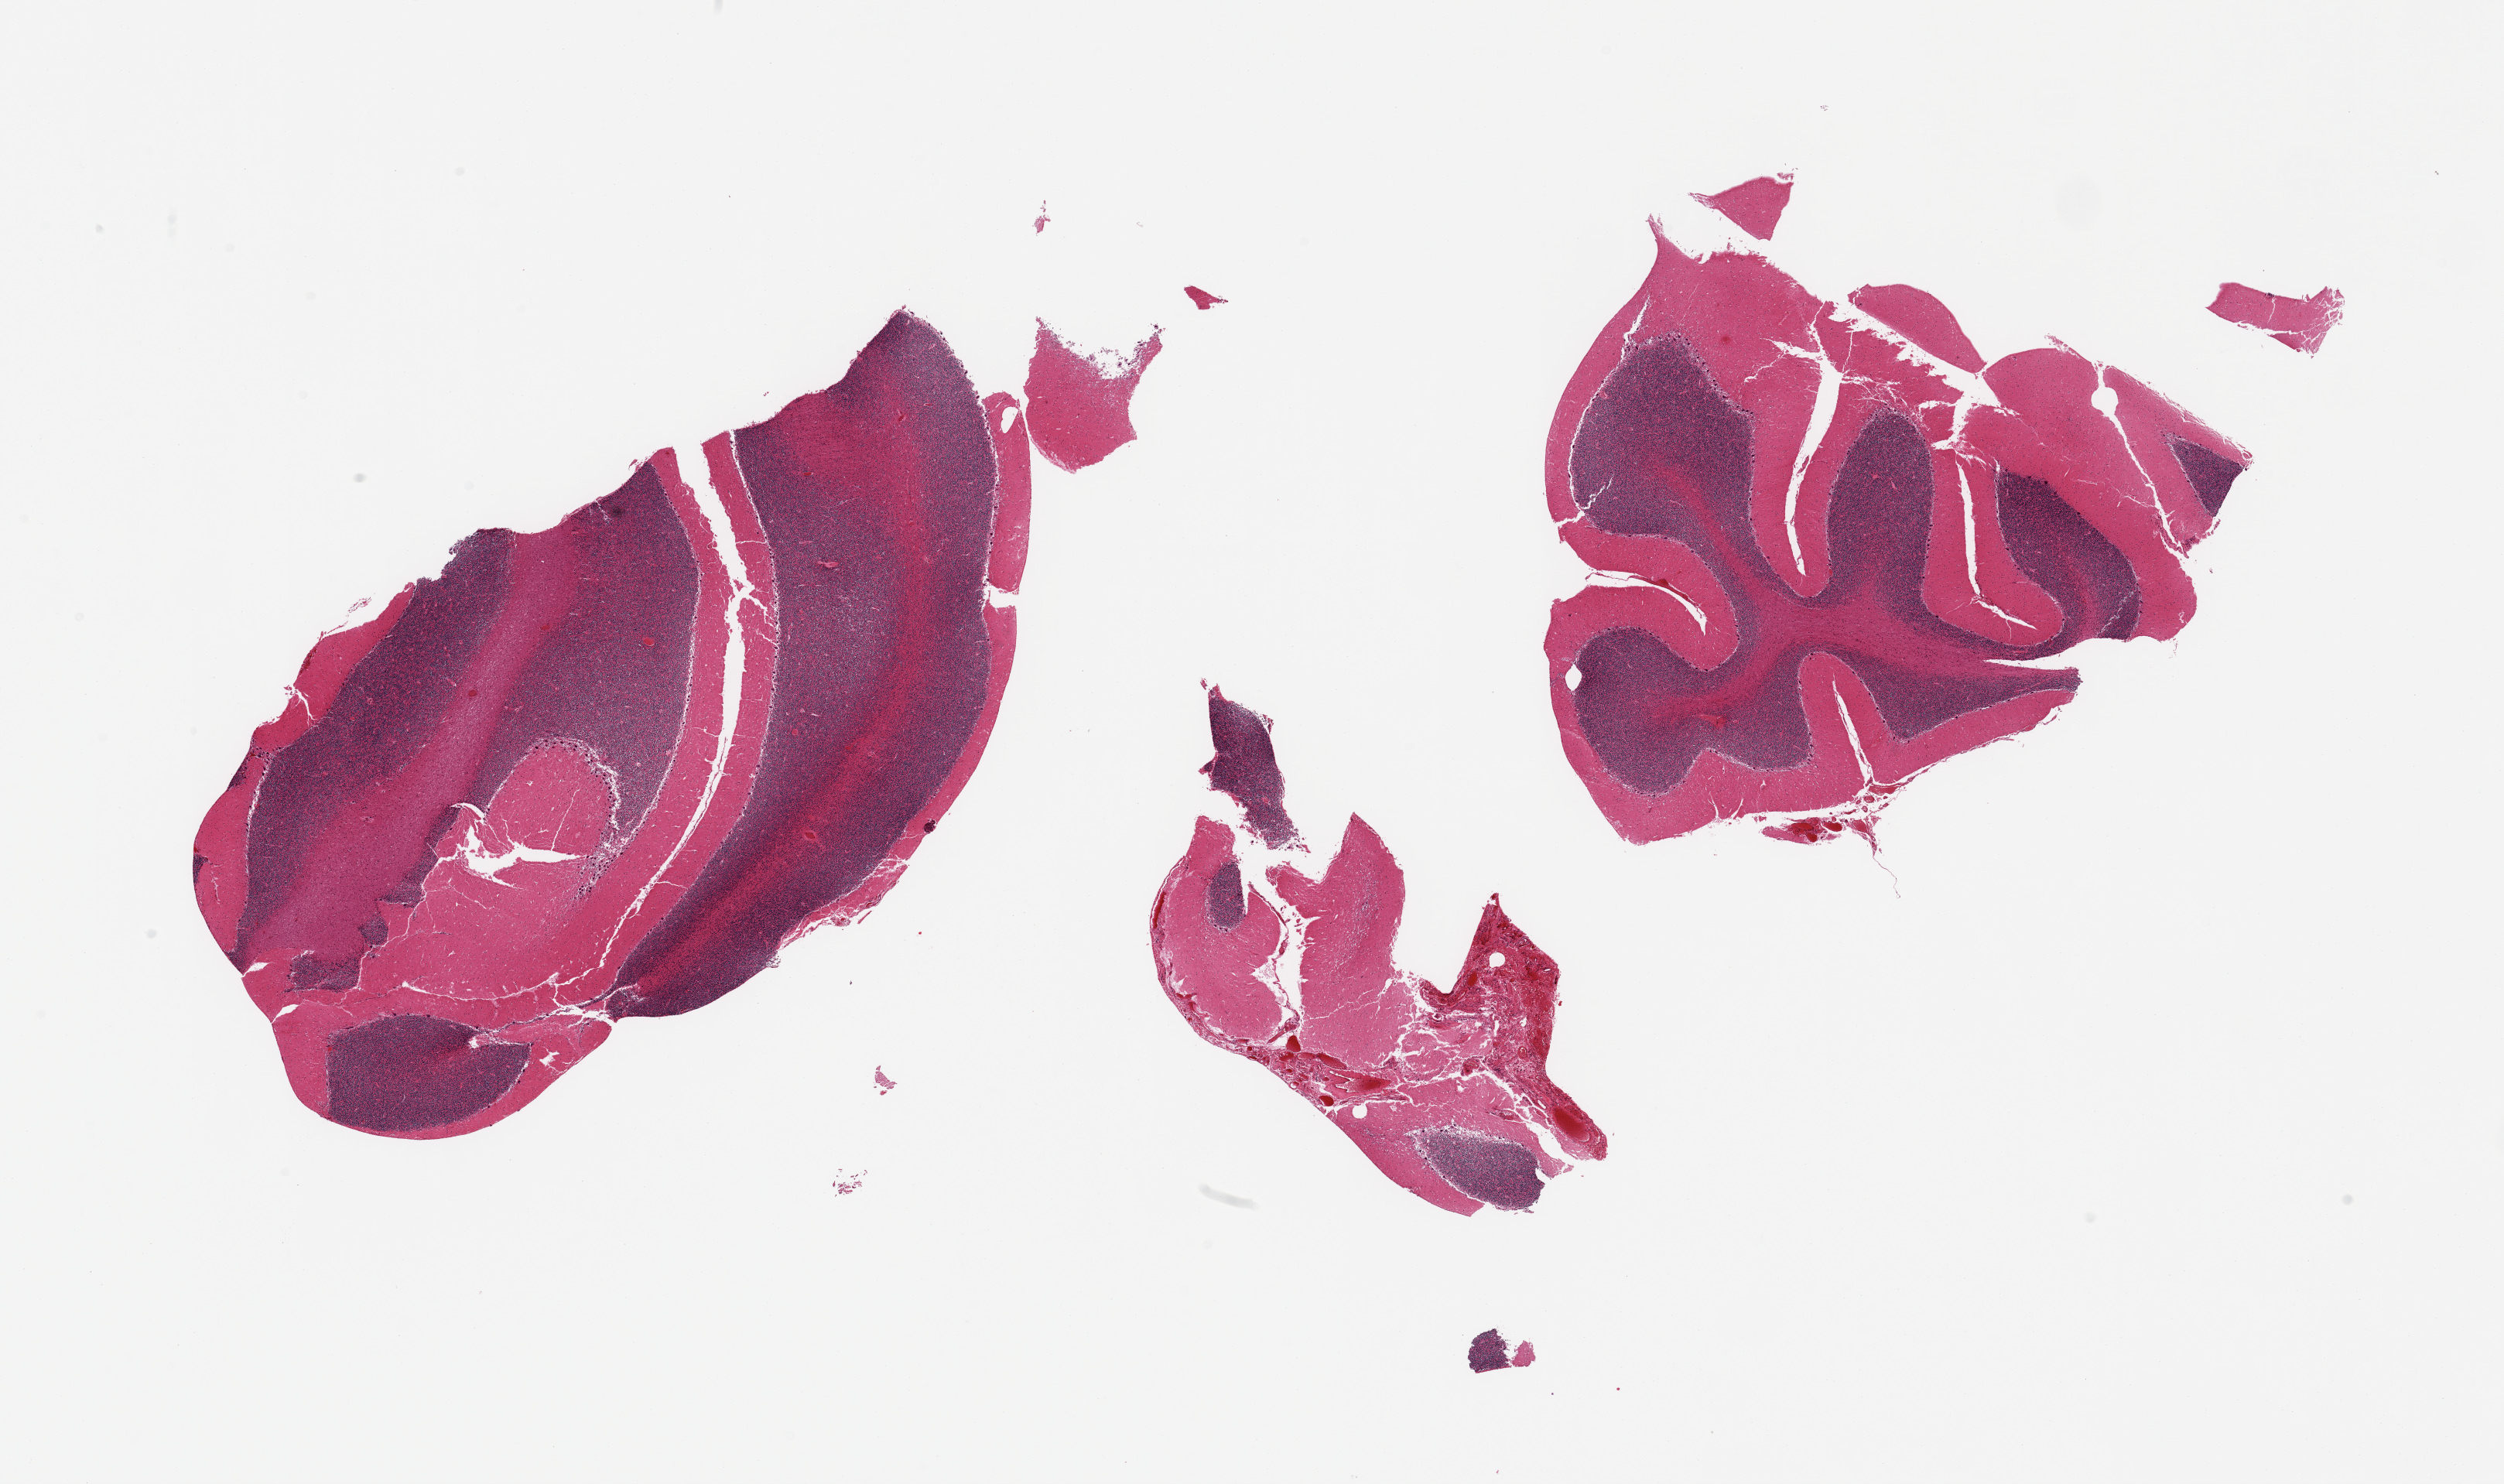
Digitized haematoxylin and eosin-stained section, brightfield, low-resolution overview of the scanned area, about 25.6 x 15.2 mm; PAXgene-fixed, paraffin-embedded tissue; target tissue: cerebellum; donor tissue sample. Female donor.
Pathologist's review note for this sample: 3 pieces (fragmented); Purkinje cells well visualized, fragments of meninges present.